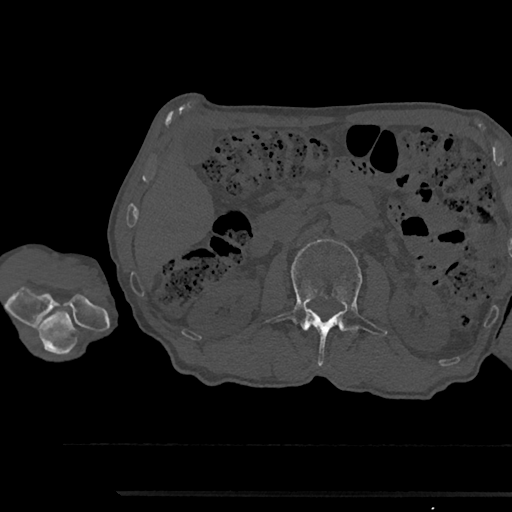
CT including the spine, one axial slice. Position 570 of 797 along the scan axis. Reconstruction kernel Br40s/3. Bone window (W 1800 / L 400 HU). 0.5 mm slice thickness. 512 × 512 image matrix. Patient: male, 79 years. From the clinical record (not read from this slice): primary cancer: prostate.
Outlined on this slice (semi-automatically segmented with operator editing):
- L2 vertebra: box from (x=265, y=239) to (x=387, y=366) px